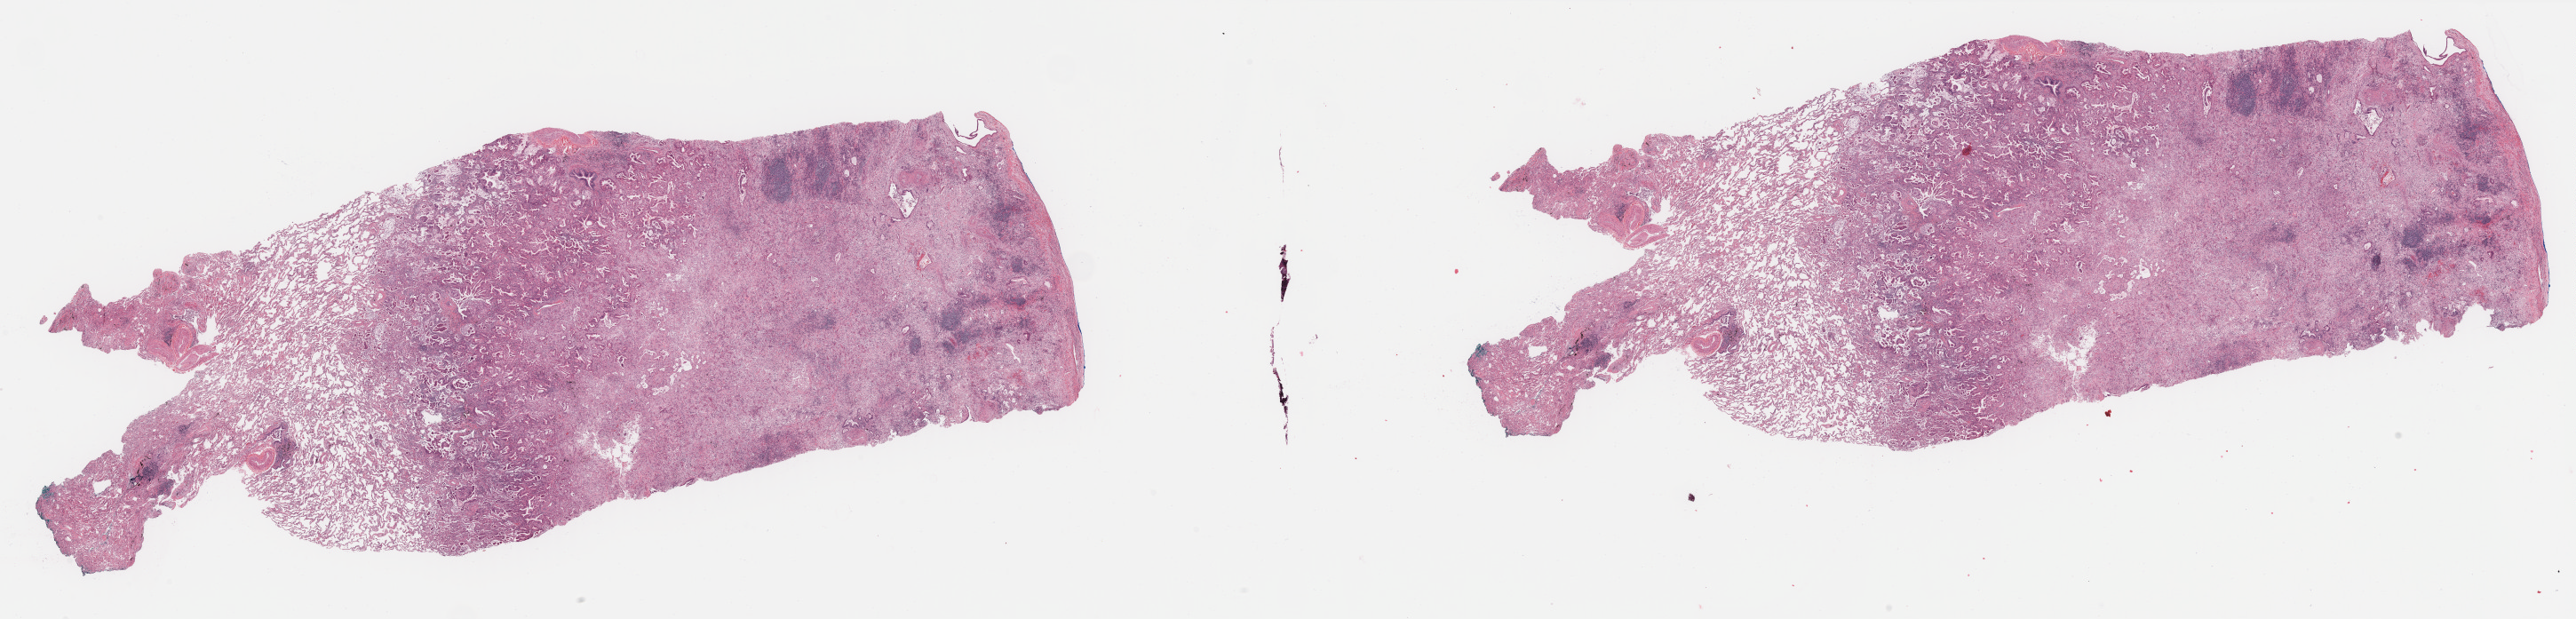
H&E whole-slide image, whole scanned area (about 45.9 x 11.0 mm) shown as a low-resolution overview. FFPE section. Lung, primary tumour sample. Patient: male, age at initial diagnosis 80 years.
Histologic diagnosis: Acinar cell carcinoma (upper lobe, lung).